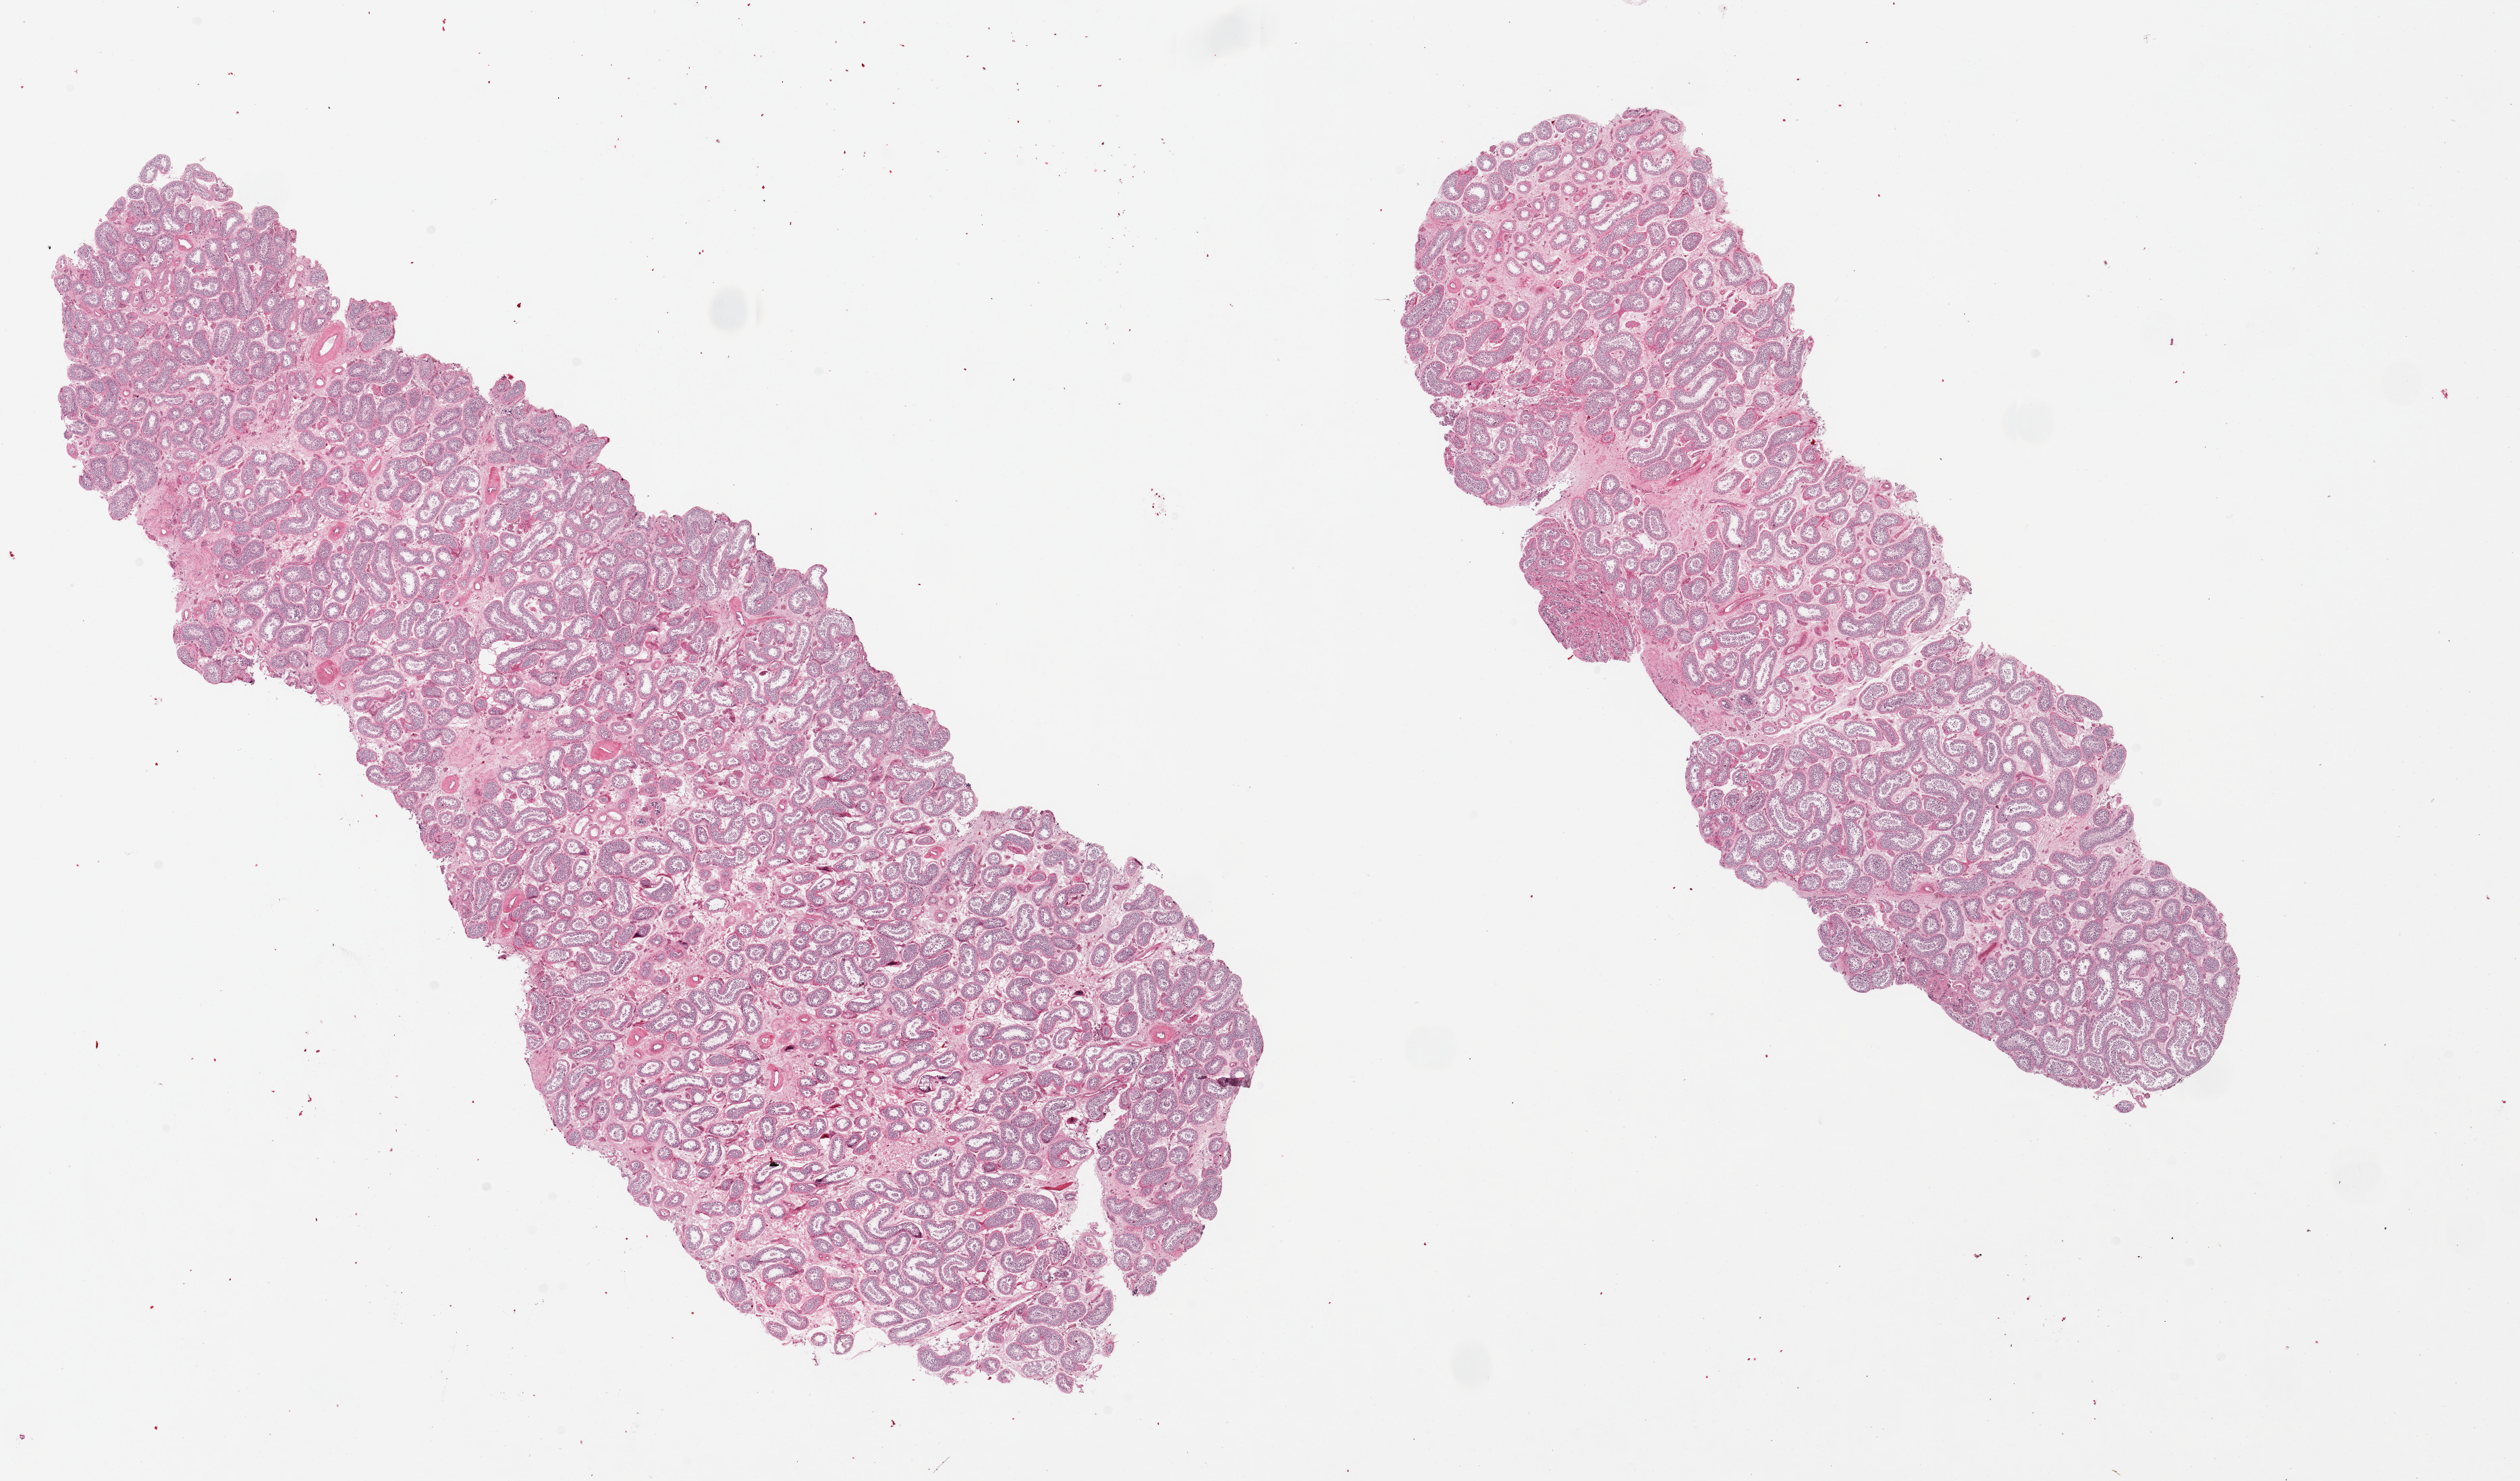
Digitized hematoxylin and eosin (H&E)-stained section, brightfield — shown as a low-resolution overview of the whole scanned area (about 29.5 x 17.4 mm); PAXgene-fixed paraffin-embedded (PFPE) section; sampled site (target tissue): testis; tissue donor sample. Male donor.
• pathologist's review note for this sample: 2 pieces, active spermatogenesis, some vascular thickening and tubular hyalinization